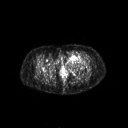
FDG PET of an extremity soft-tissue mass (from a PET/CT study), one axial slice; position 43 of 267 along the scan axis; 3.27 mm slice thickness; 128 × 128 image matrix, field of view 700 × 700 mm. Patient: female, 47 years. From the clinical record (not read from this slice): histological type: myxofibrosarcoma; grade: intermediate; site of the primary tumour: left thigh.
Outlined on this slice (expert contour drawn on MRI and transferred to this co-registered scan by the dataset authors):
- gross tumour volume including surrounding oedema: bounding box (x1, y1, x2, y2) in pixels: (65, 54, 83, 64)
- gross tumour volume (mass): (68, 54, 78, 61)